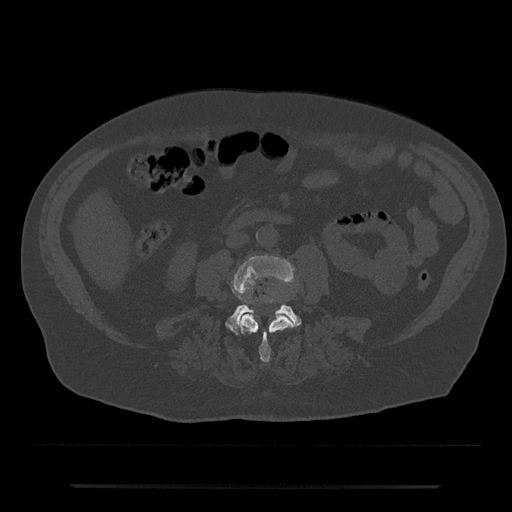
CT including the spine, one axial slice; slice 382 of 797 in the series (ordered by position); 120 kVp; bone window (W 1800 / L 400 HU); 0.5 mm slice thickness; 512 × 512 image matrix, field of view 434 × 434 mm. Male patient, age 80 years. From the clinical record (not read from this slice): primary cancer: prostate; vertebrae with lytic lesions (as recorded): L1, T11.
Structures marked on this image (semi-automatic segmentation, software-assisted and operator-edited):
- L3 vertebra: box from (x=232, y=255) to (x=296, y=362) px
- L4 vertebra: (x=225, y=297)–(x=301, y=335)